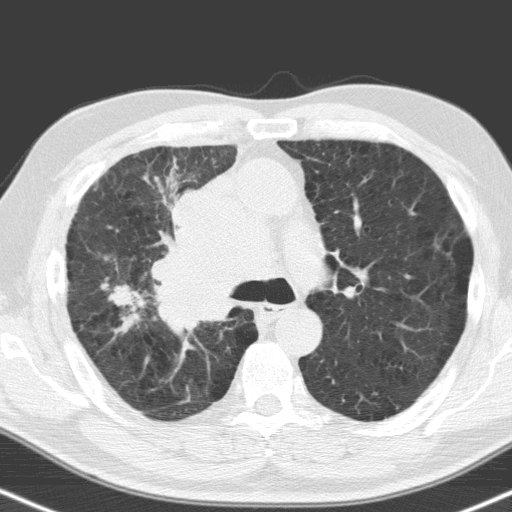
Chest CT (low-dose screening protocol), one axial image. Baseline screening round. Lung window (W 1500 / L -600 HU). Standard (soft-tissue) reconstruction kernel (C). 120 kVp. Slice 52 of 160 in the series. Male, age 71 years at enrolment.
- Expert-annotated lung lesion, bounding box <83,270,153,341> (left, top, right, bottom; pixels).
- The screening reader recorded 2 non-calcified nodules or masses ≥4 mm on this exam (right upper lobe, right upper lobe); which of them this box marks is not recorded.
- Official screen result: positive, change unspecified: nodule(s) >= 4 mm or enlarging nodule(s), mass(es), or other non-specific abnormalities suspicious for lung cancer.
- Participant outcome: lung cancer diagnosed 31 days after this screen — small cell carcinoma, NOS, right upper lobe, stage IV (AJCC 6th edition), 40 mm at pathology.